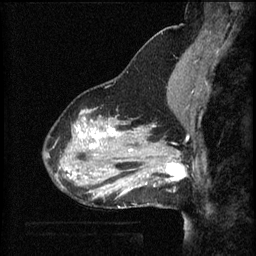
Breast MRI (dynamic contrast-enhanced), one sagittal slice. Position 20 of 60 along the scan axis. 3 images stored at this slice position (order not interpretable as contrast timing). 1.5 T. TE 4.2 ms, TR 8.2 ms. 2 mm slice thickness. 256 × 256 image matrix, field of view 200 × 200 mm. Female patient, age 37 years.
Annotated regions visible in this slice (semi-automatically segmented with operator editing):
- analysis volume of interest (the breast-tissue region the enhancement analysis was run in; not a lesion): bounding box <148,140,191,187> (left, top, right, bottom; pixels)
- tumour enhancement mask (voxels above the 70 % enhancement threshold inside the analysis volume of interest): <158,152,187,183>